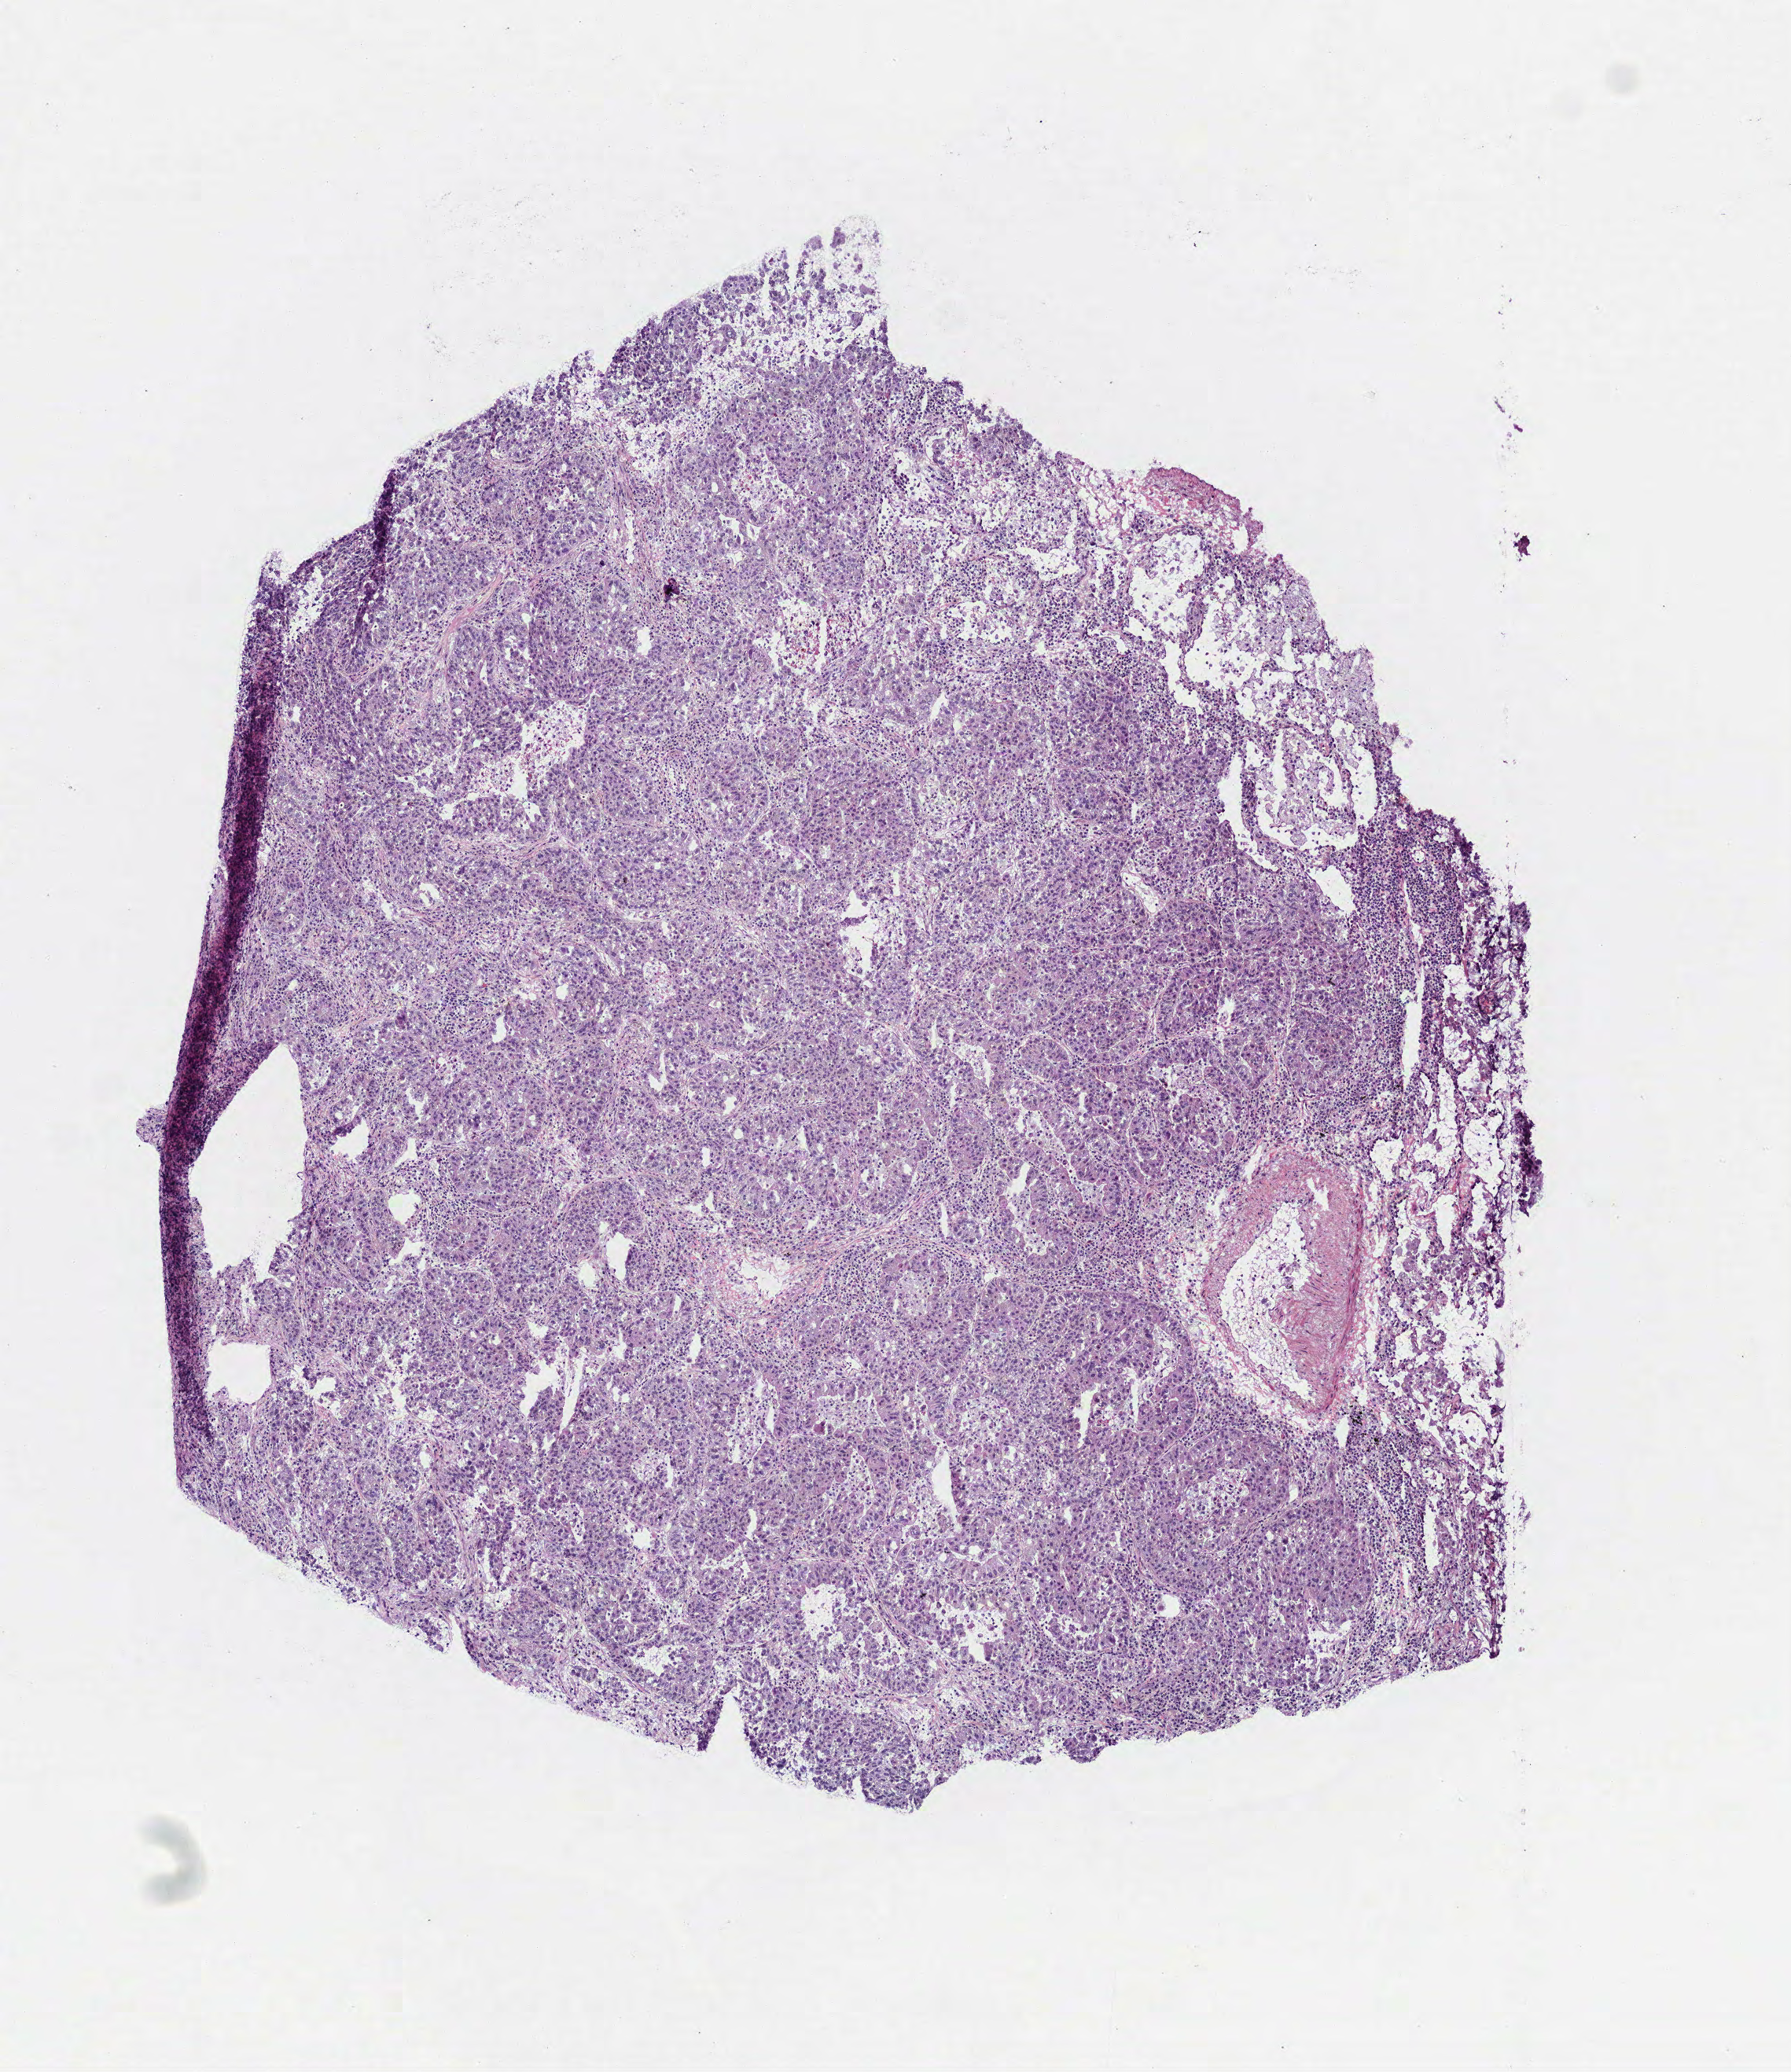
H&E-stained whole-slide image — shown as a low-resolution overview of the whole scanned area (about 4.6 x 5.3 mm, acquisition: 40x scan), frozen section from the top of the tissue portion, sample: primary tumour, lung. Patient sex: female. Composition of this section per pathologist review: tumour cells 80%, tumour nuclei 65%, normal cells 2%, stromal cells 15%, necrosis 3%. Inflammatory infiltration, as recorded: lymphocyte infiltration 20%, monocyte infiltration 10%, neutrophil infiltration 0%.
TNM: T2 N0 M0. Histologic diagnosis: Adenocarcinoma, NOS (upper lobe, lung). Laterality: right. AJCC pathologic stage: IB (6th edition).